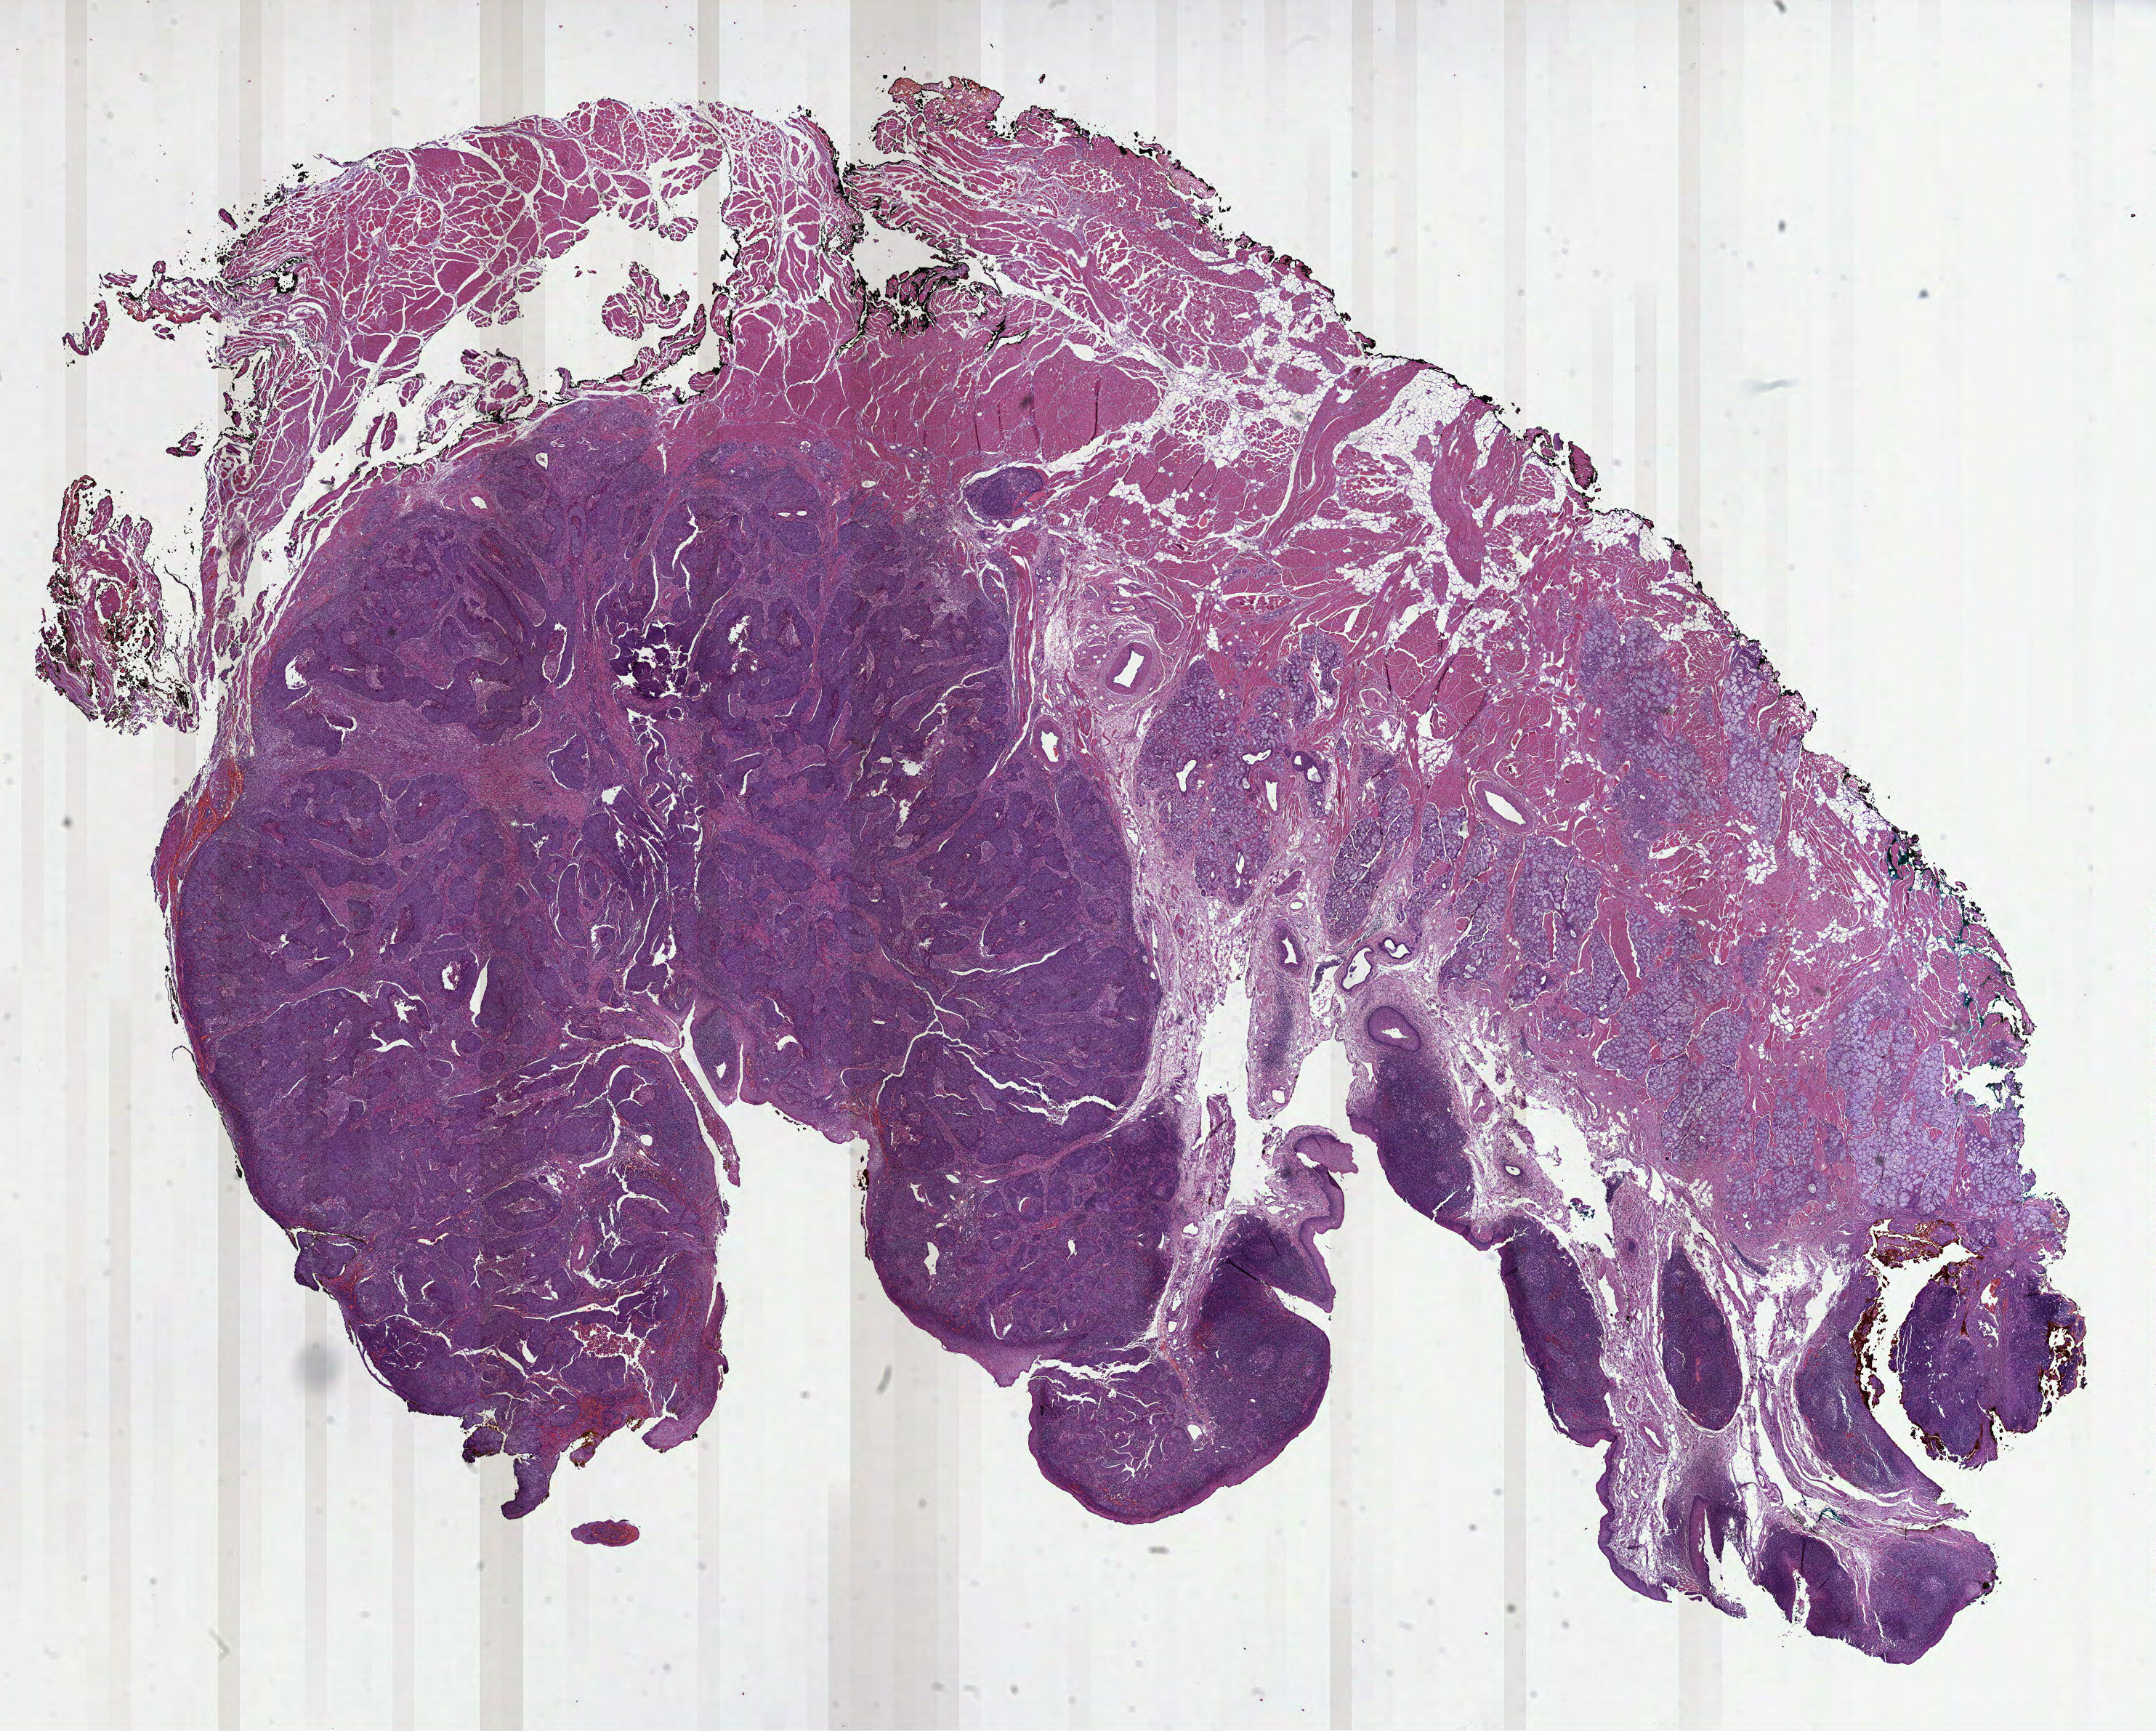
Digitized H&E tissue section (whole slide) — shown as a low-resolution overview of the whole scanned area (about 23.9 x 19.2 mm, from a 40x scan); formalin-fixed paraffin-embedded (FFPE) diagnostic section; primary tumour sample from the head and neck. Patient: male, age at initial diagnosis 58 years. Histologic grade: G4 (undifferentiated).
Laterality: left. Pathologic diagnosis: Basaloid squamous cell carcinoma (base of tongue, NOS). AJCC pathologic stage: III (7th edition). TNM: T1 N1.